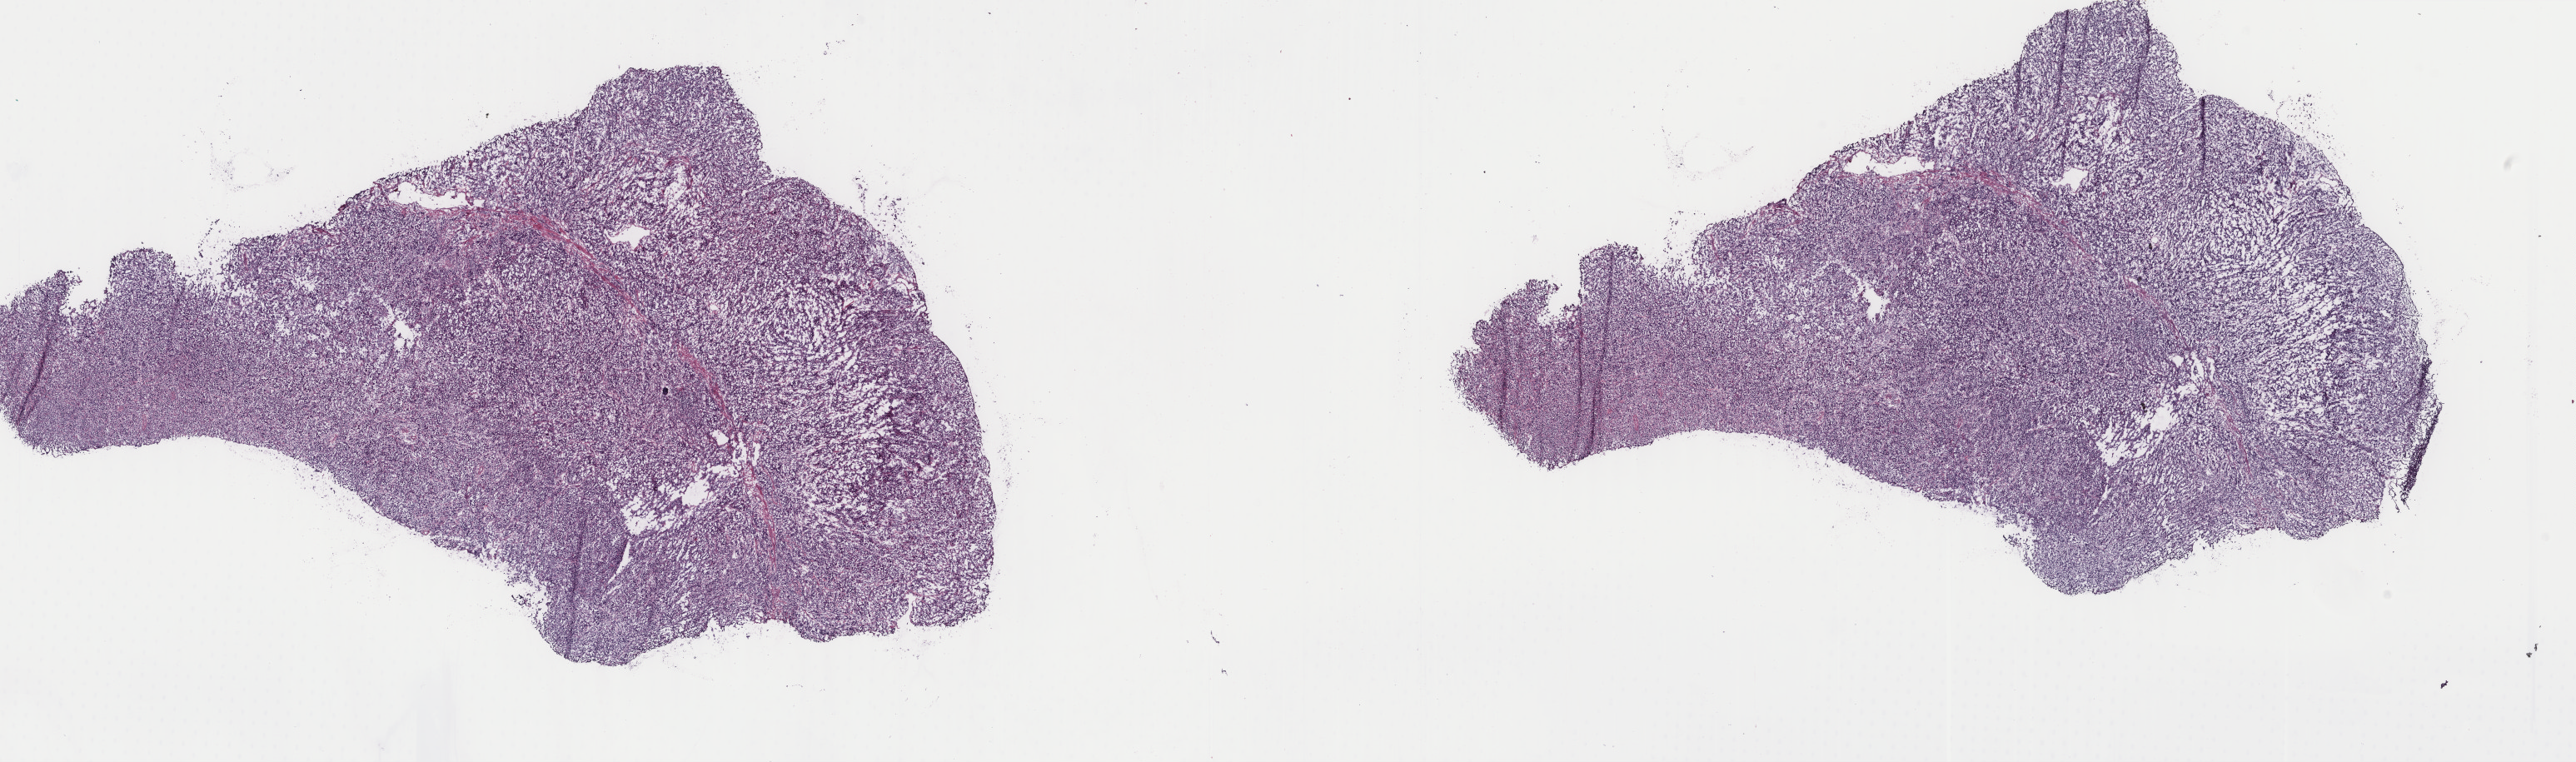
Digitized H&E tissue section (whole slide) — whole scanned area (about 24.6 x 7.3 mm, acquisition: 40x scan) shown as a low-resolution overview. Frozen section from the top of the tissue portion. Sample: primary tumour, stomach. Male patient; age at initial diagnosis 72 years. Slide review estimates, as recorded: tumour cells 95%, tumour nuclei 100%.
Histologic diagnosis: Carcinoma, diffuse type (body of stomach).